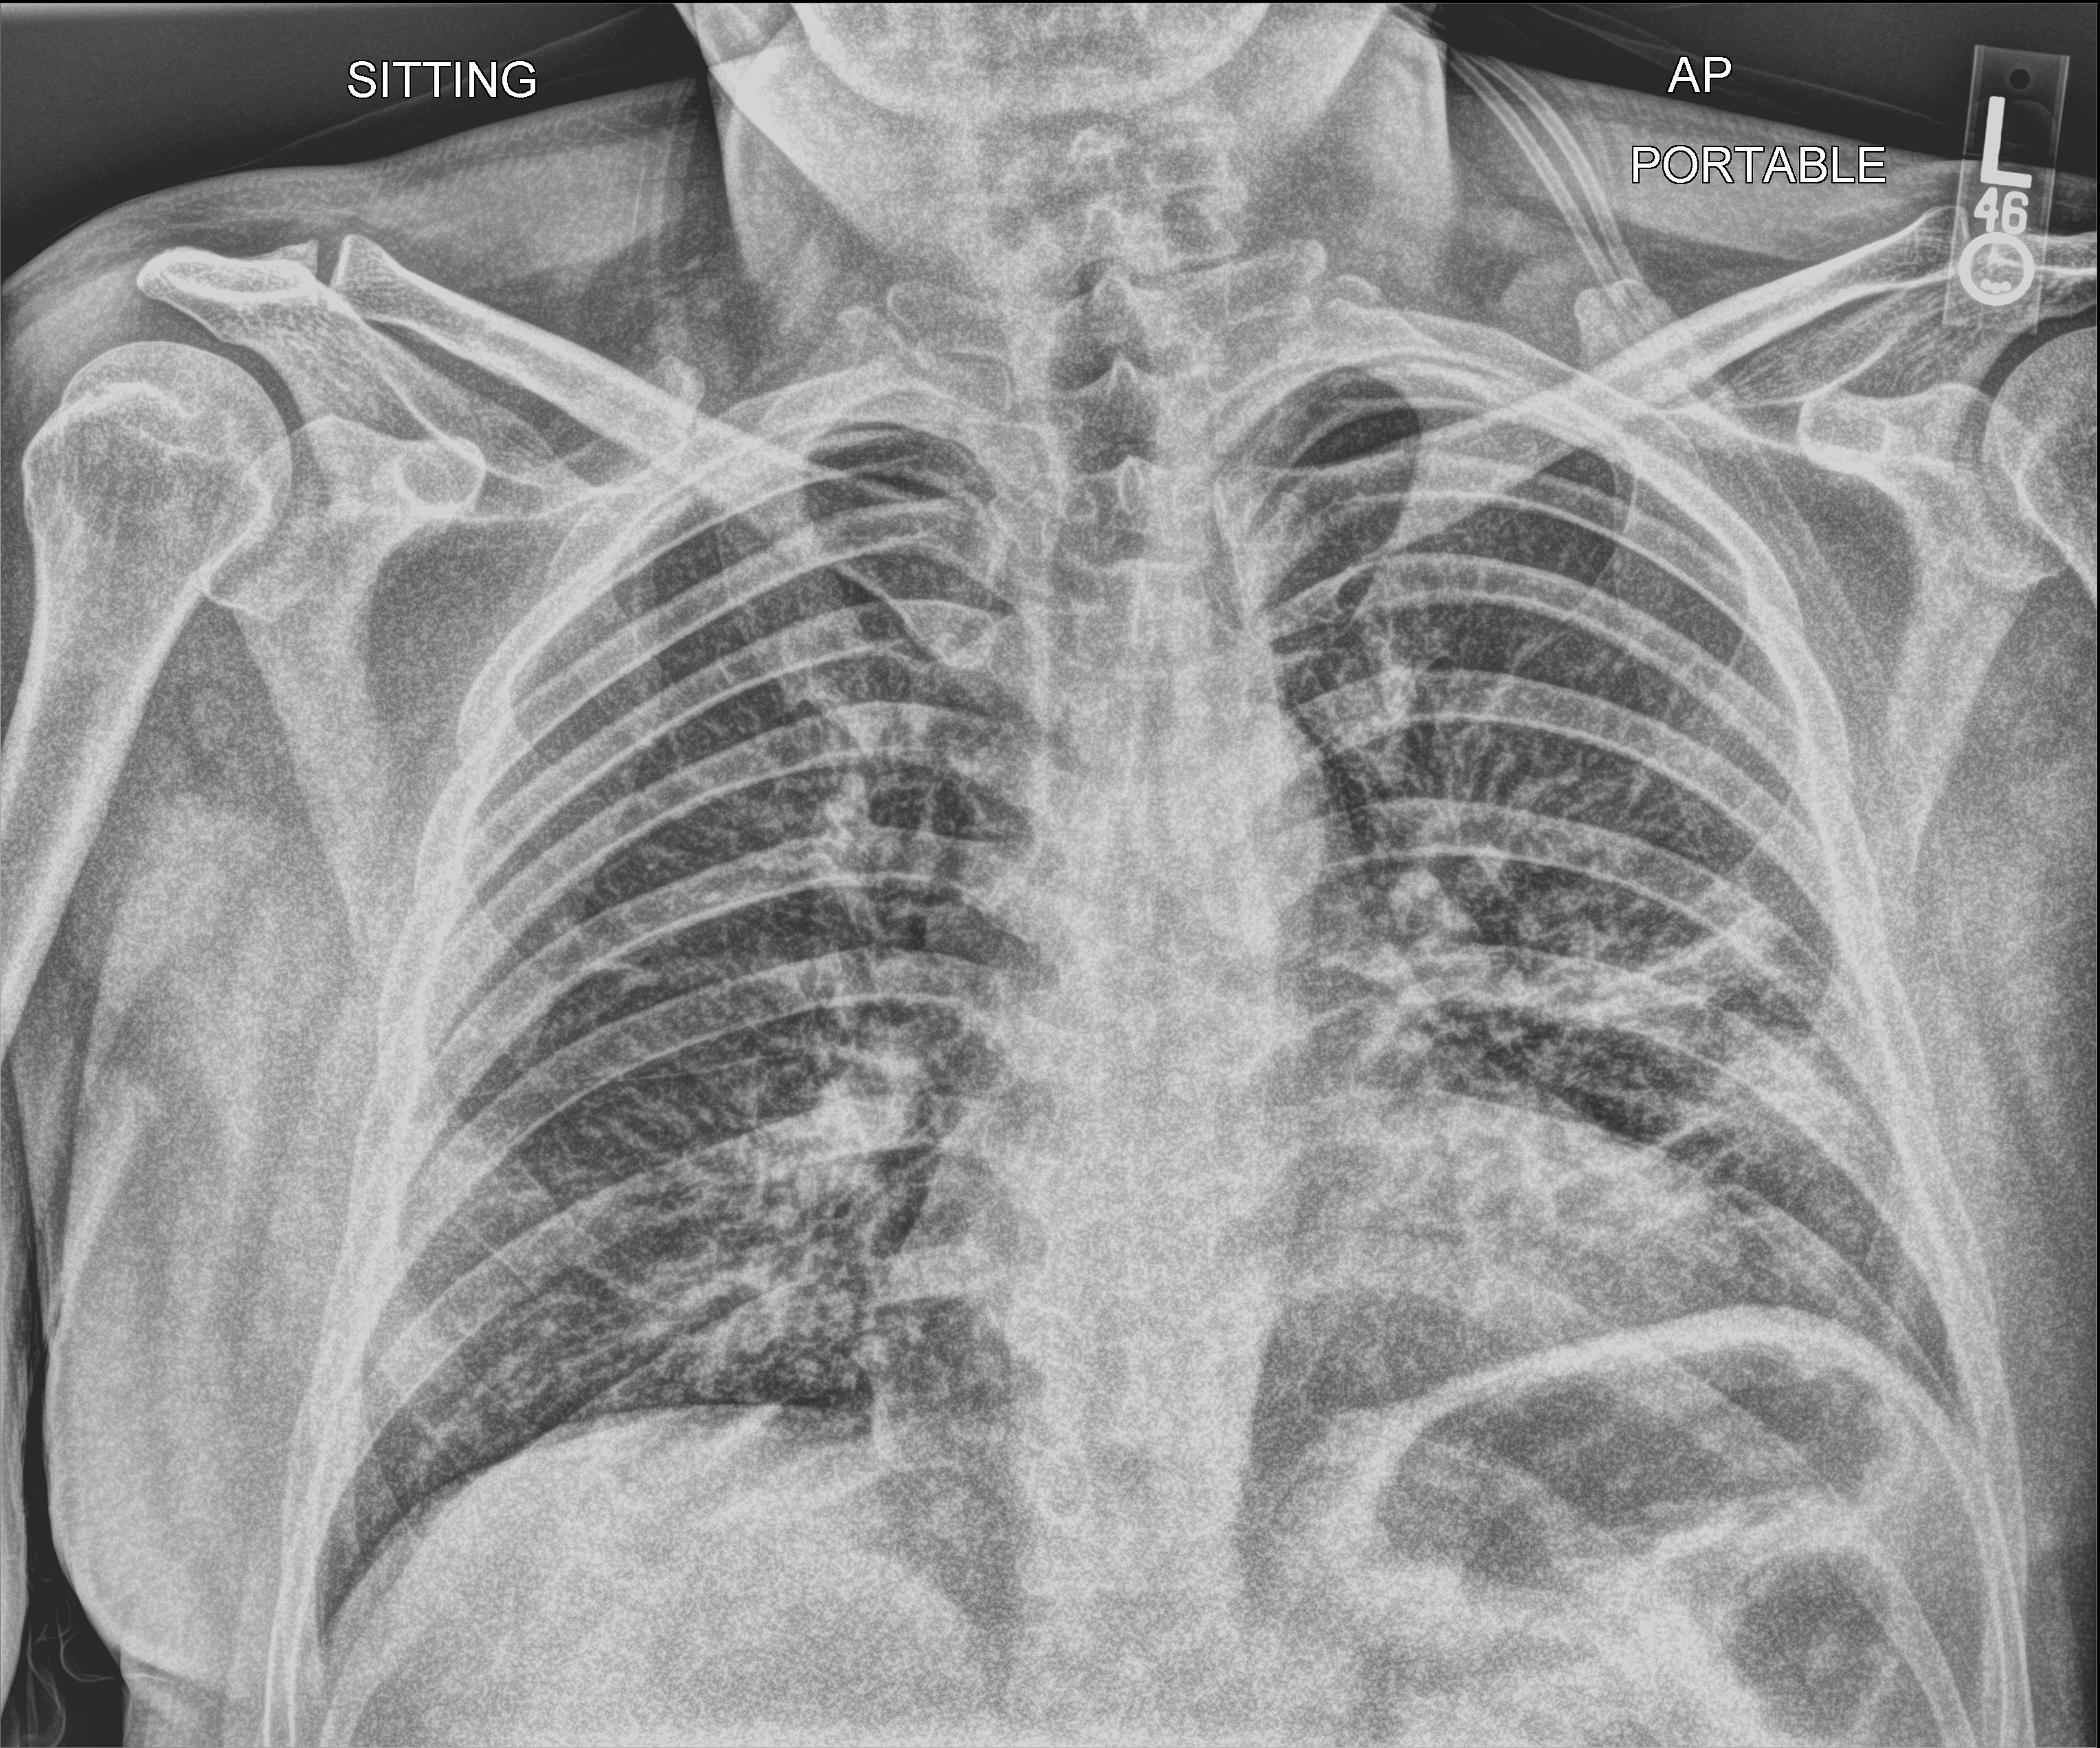
Bedside chest radiograph (computed radiography), anteroposterior (AP) projection. Patient hospitalised with COVID-19; male, aged 18–59 years.
Admission-level facts for this patient (not findings on this image; timing relative to this image not recorded):
- admitted to intensive care during this hospital stay: no